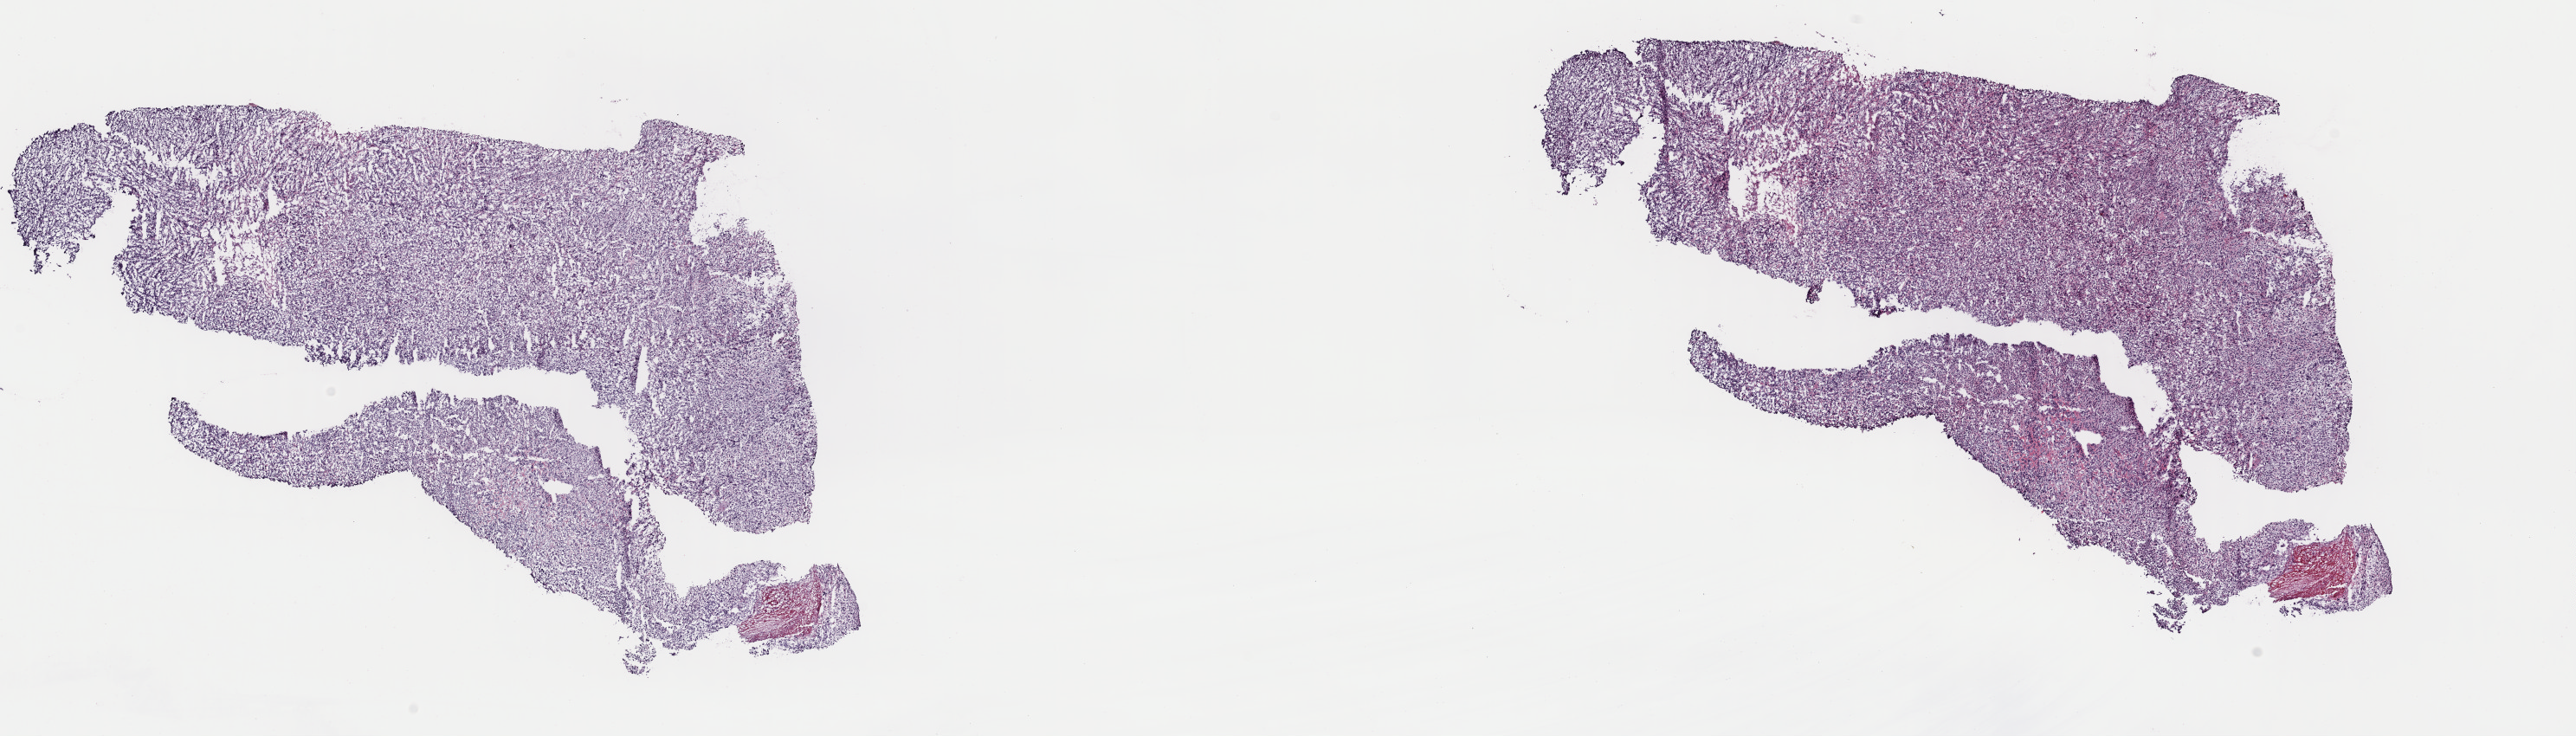
Whole-slide histology image, Hematoxylin and eosin (H&E) stained — whole scanned area (about 23.5 x 6.7 mm, acquisition: 40x scan) shown as a low-resolution overview. Frozen section from the top of the tissue portion. Sample: primary tumour, uterus. Female patient; age at initial diagnosis 59 years. Pathologist review of this section (percent, as recorded): tumour cells 90%, tumour nuclei 90%, normal cells 0%, stromal cells 10%, necrosis 0%. Infiltration values recorded for this section: lymphocyte infiltration 40%, monocyte infiltration 20%, neutrophil infiltration 20%.
FIGO stage: II. Pathologic diagnosis: Mullerian mixed tumor.